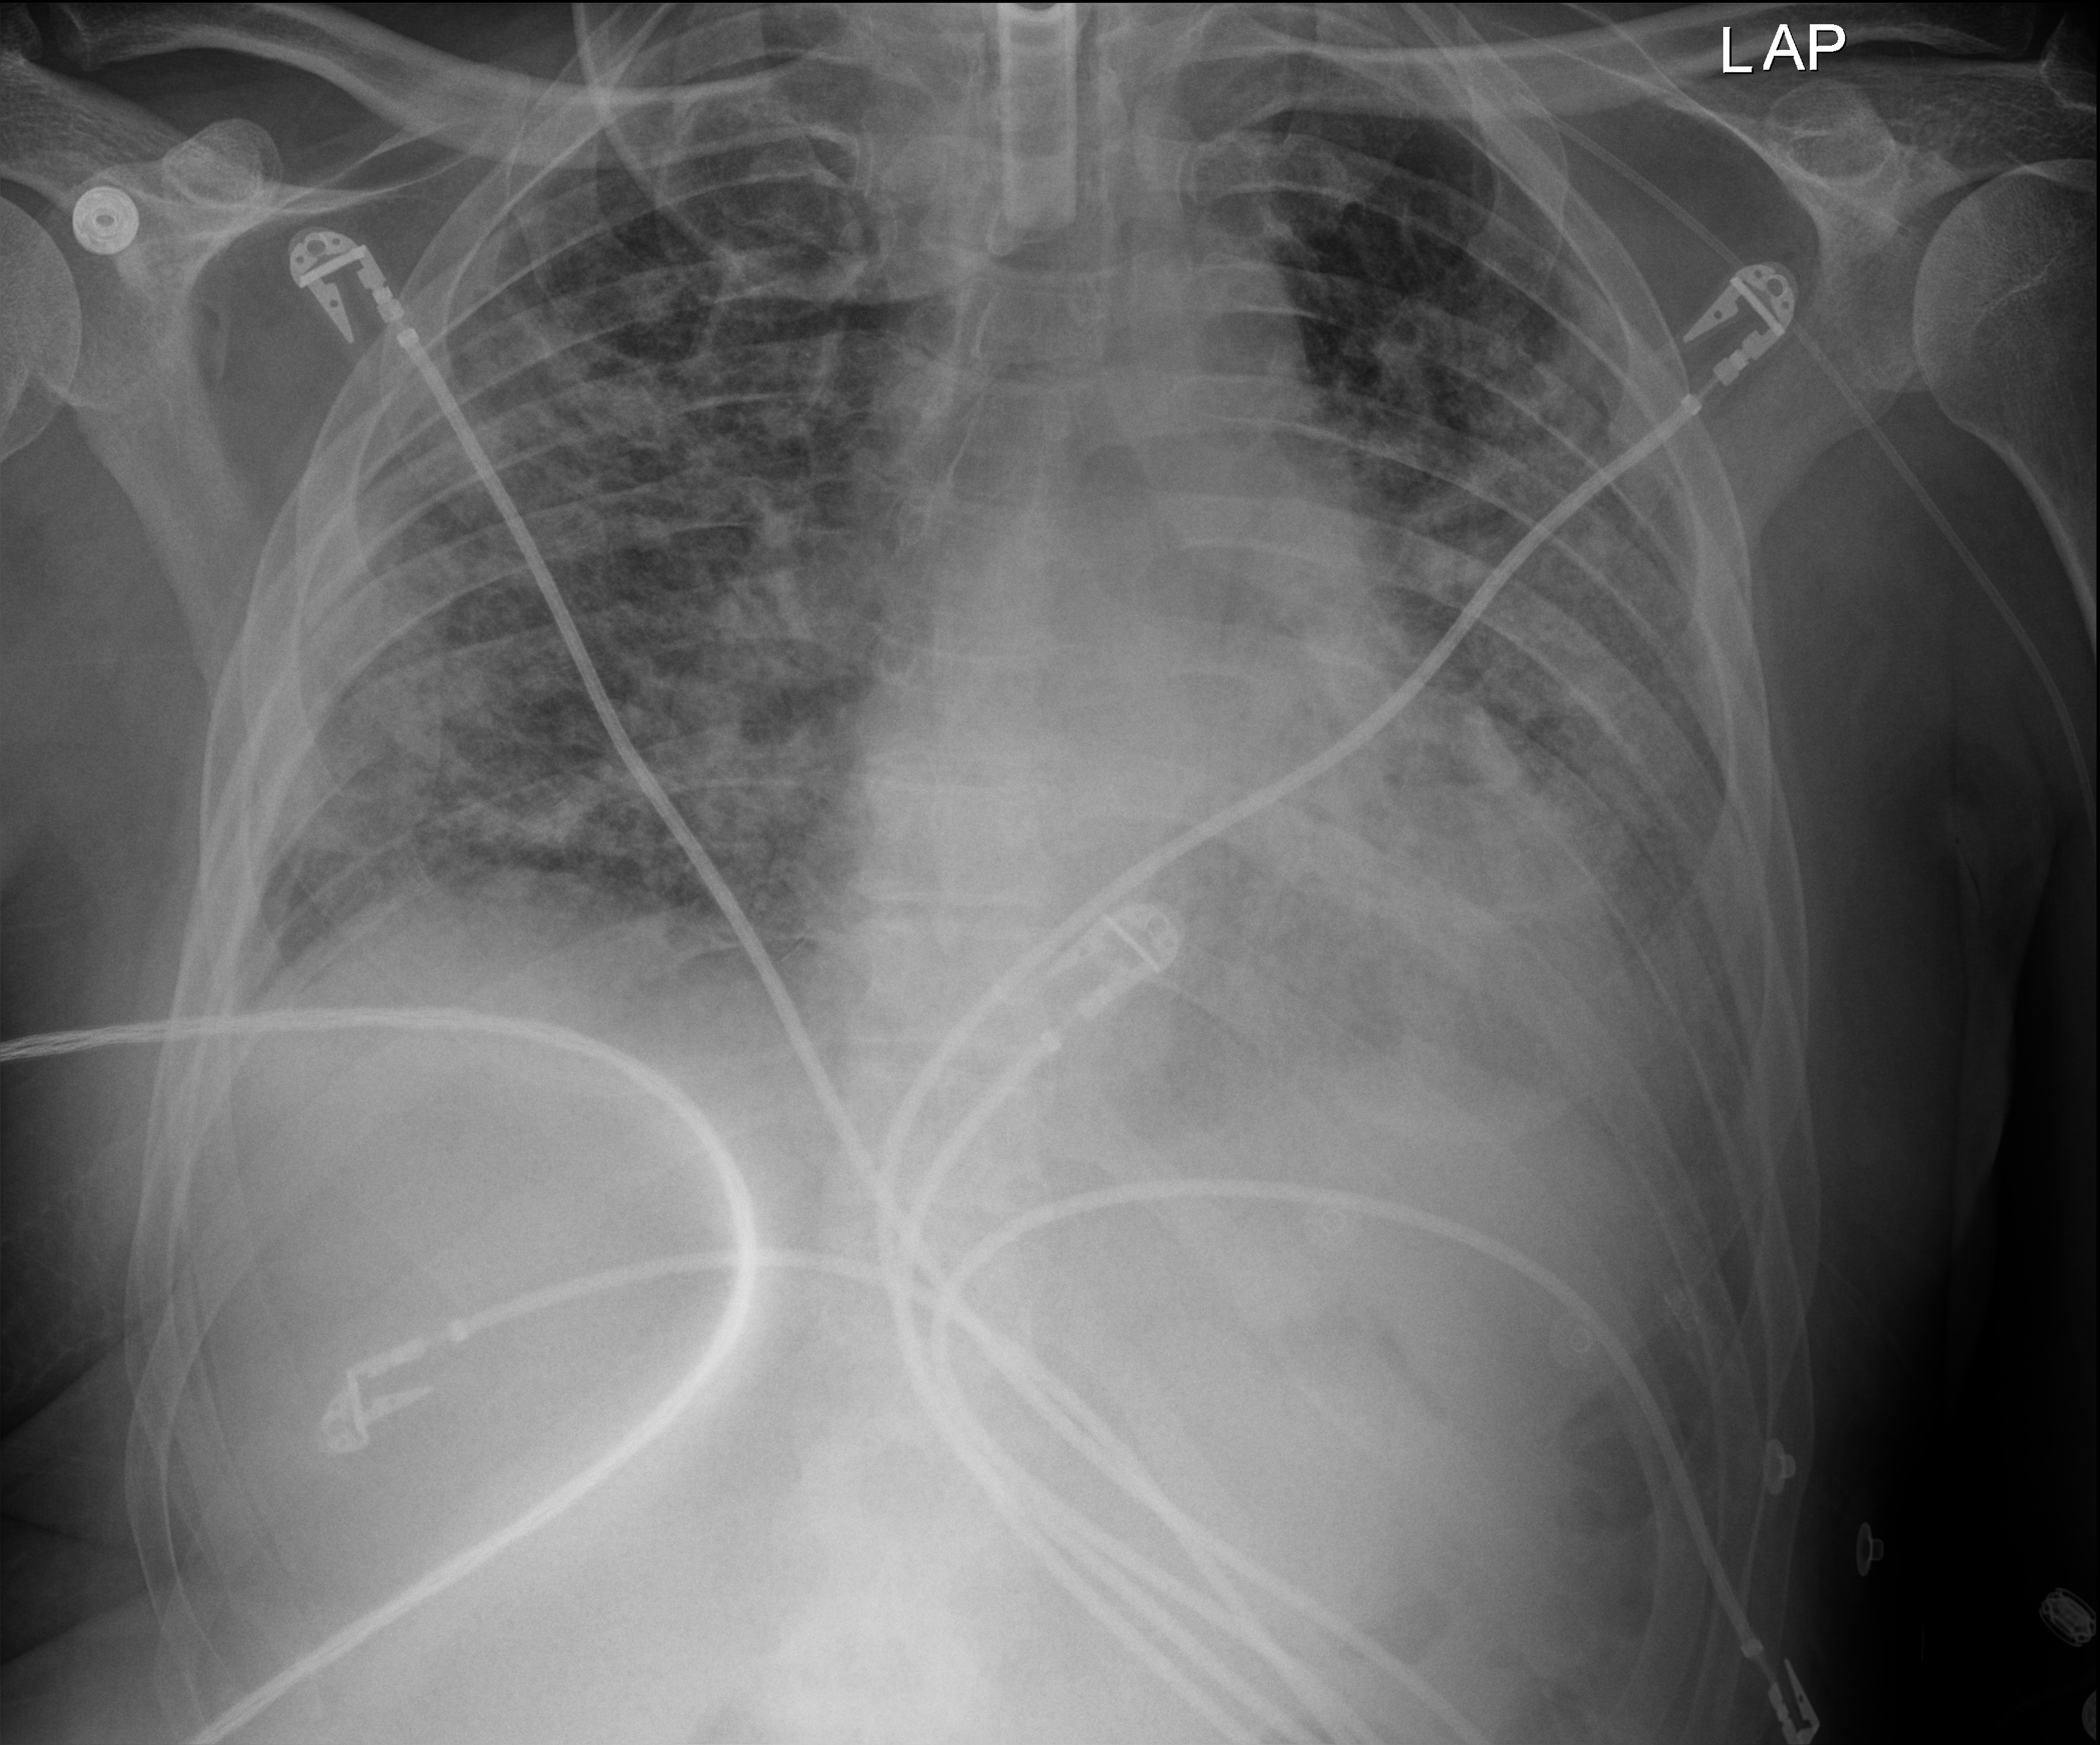
Portable chest radiograph, anteroposterior (AP) projection. Patient hospitalised with COVID-19; male, aged 18–59 years.
Hospital-stay facts (about this admission, not read from this image; timing relative to this image not recorded): mechanically ventilated during this hospital stay: yes; admitted to intensive care during this hospital stay: yes.